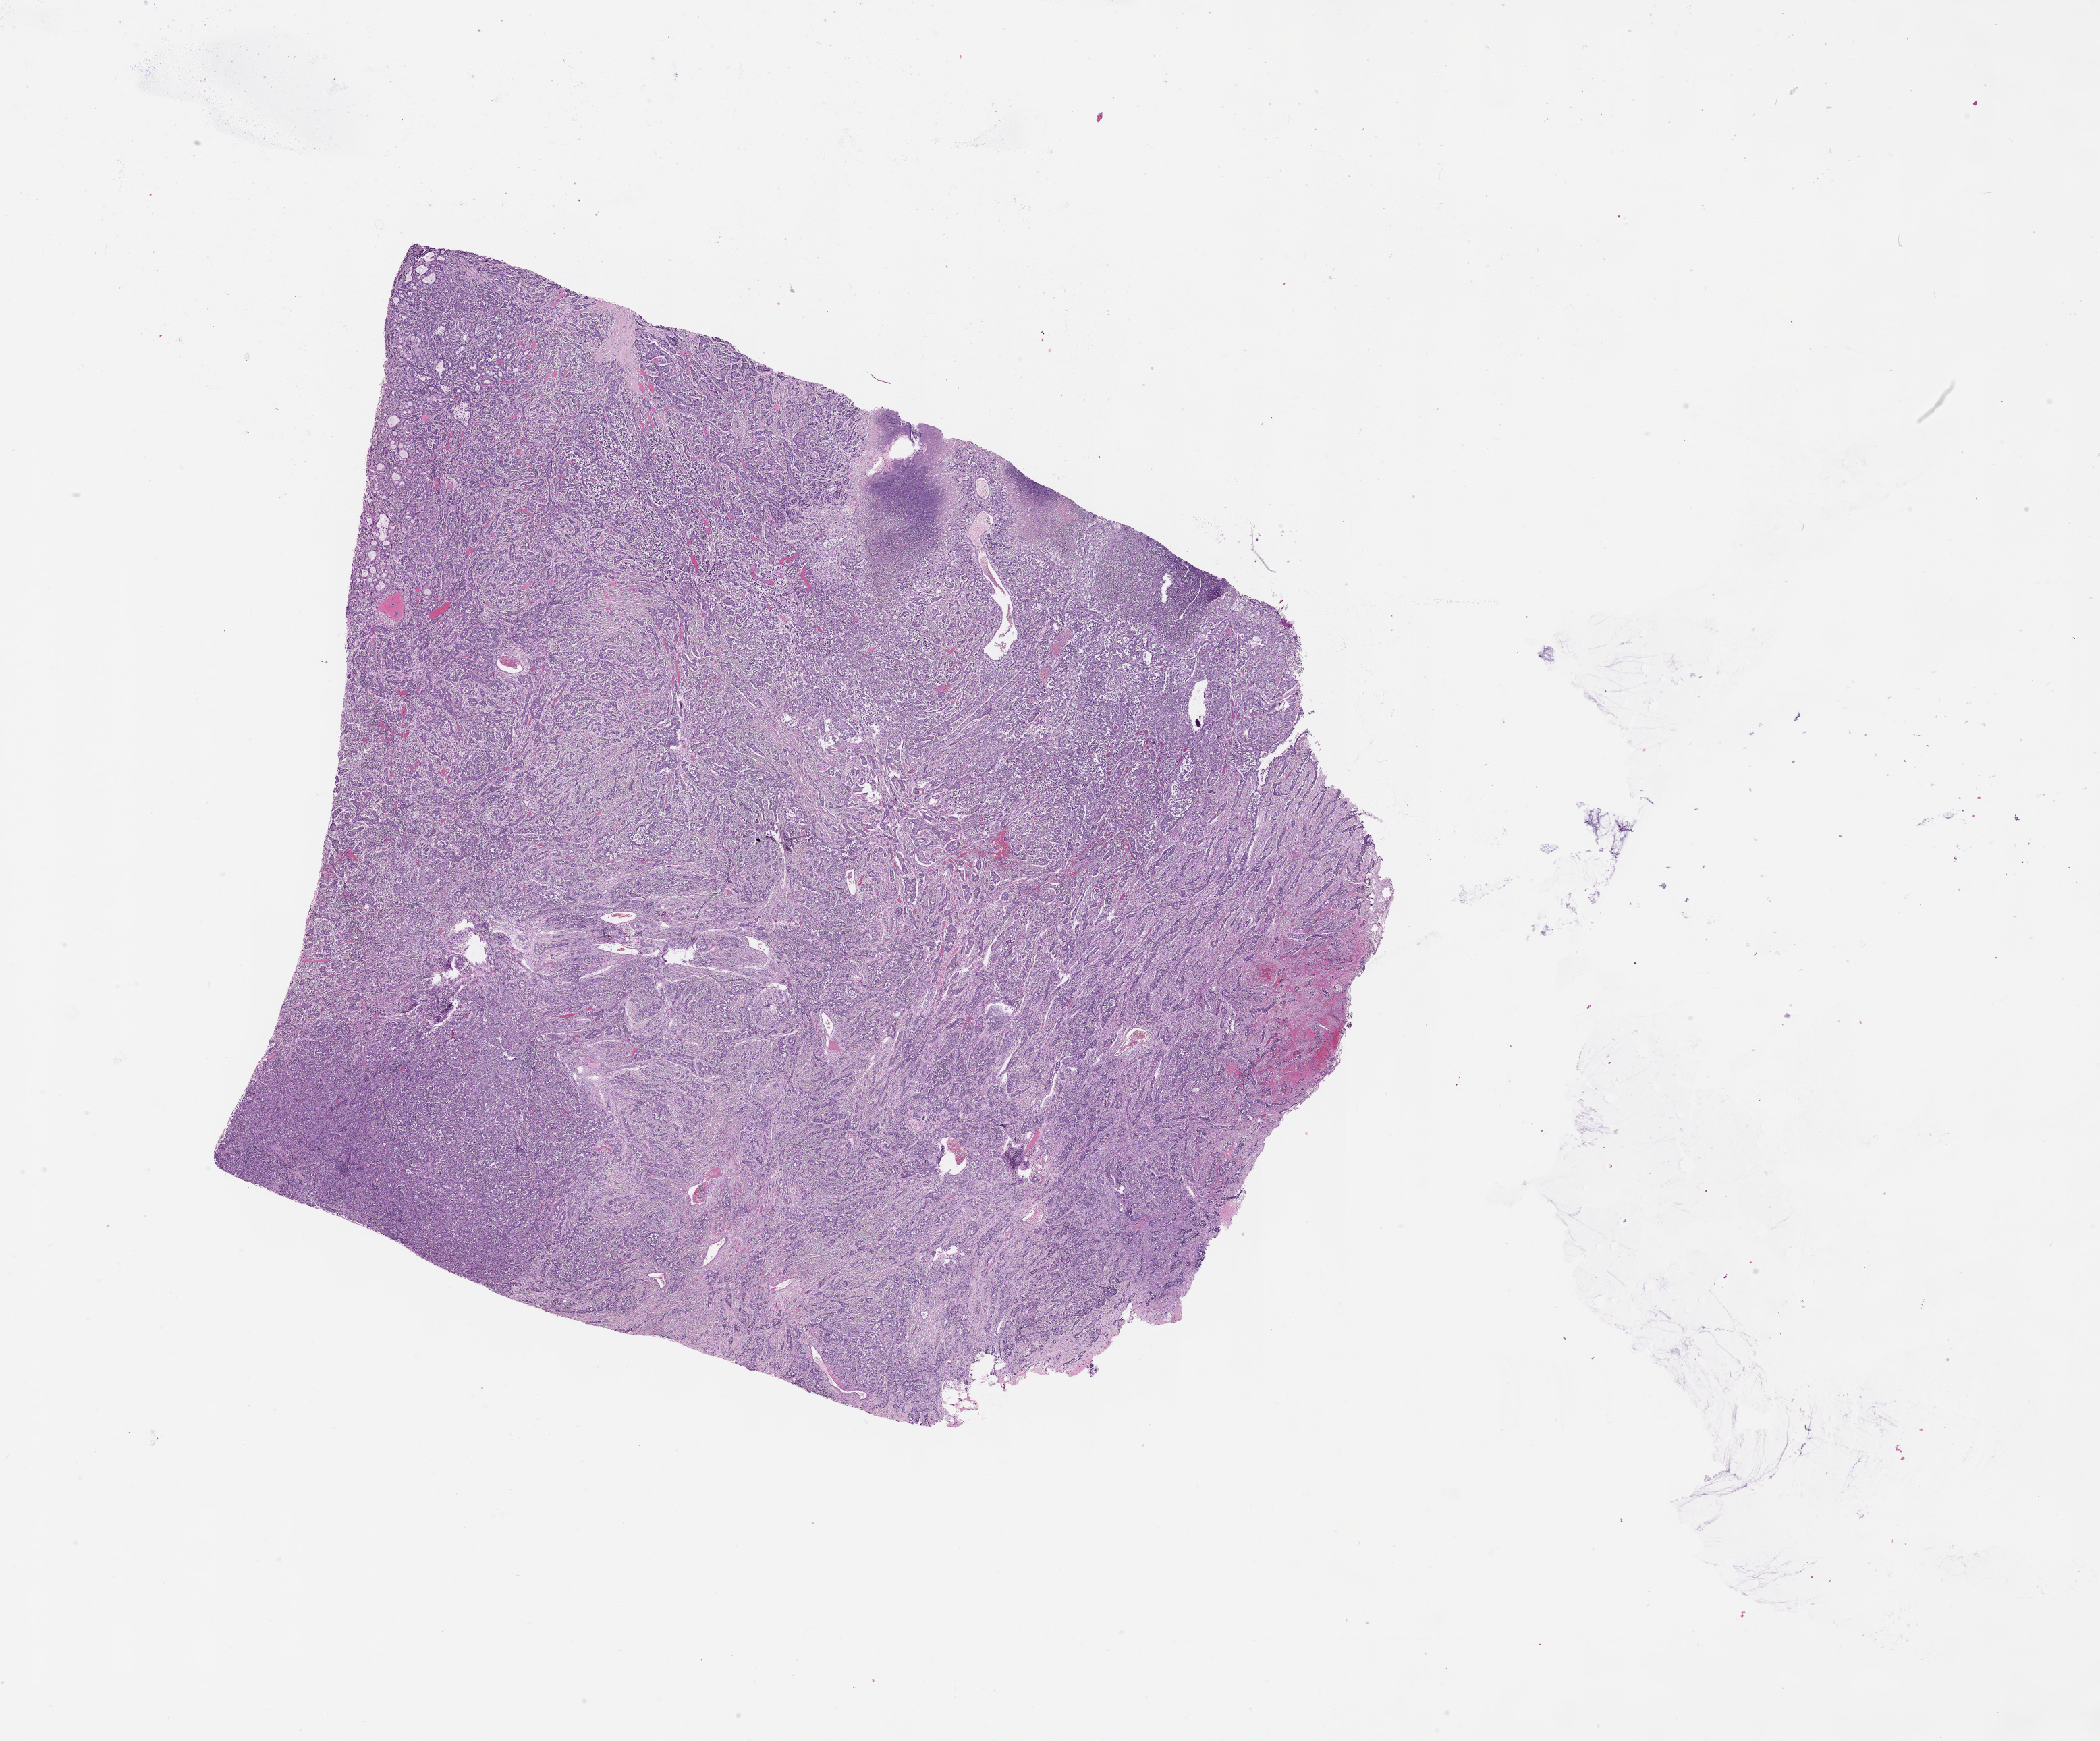
Hematoxylin and eosin (H&E) stained whole-slide image, low-resolution overview of the scanned area, about 25.1 x 20.8 mm (from a 20x scan). Lung, tissue type not recorded.
• patient diagnosis (cohort enrolment): squamous cell carcinoma (lung)